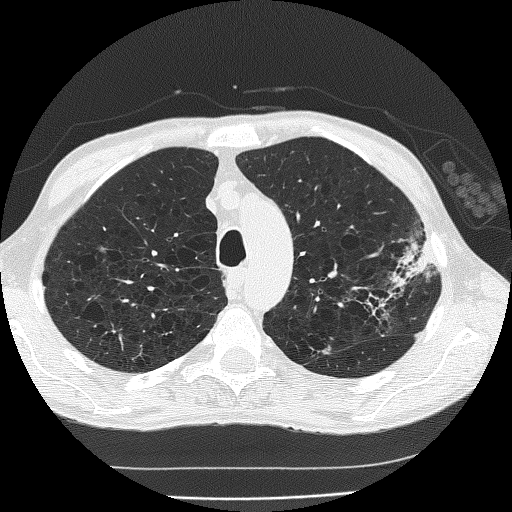
Low-dose screening chest CT, one axial slice; slice 141 of 185 in the series (ordered by position); lung window (W 1500 / L -600 HU); 2 mm slice thickness; 512 × 512 image matrix, field of view 320 × 320 mm.
Structures marked on this image (outlined manually by an expert reader):
- lesion 1 (tumor, upper lobe of left lung): bounding box (x1, y1, x2, y2) in pixels: (398, 242, 434, 277)